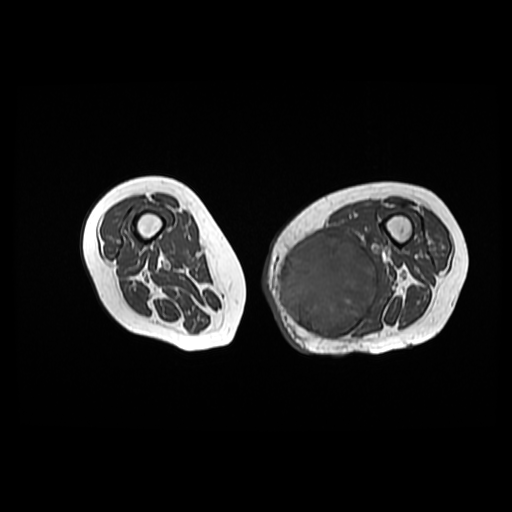
MRI of an extremity soft-tissue mass, one axial slice; slice 28 of 42 in the series (ordered by position); 6 mm slice thickness; 512 × 512 image matrix, field of view 420 × 420 mm. Female patient. From the clinical record (not read from this slice): histological type: pleomorphic leiomyosarcoma; grade: high; site of the primary tumour: left thigh.
Outlined on this slice (manually delineated by an expert):
- gross tumour volume including surrounding oedema: box from (x=277, y=233) to (x=384, y=340) px
- gross tumour volume (mass): (x=277, y=233)–(x=379, y=338)